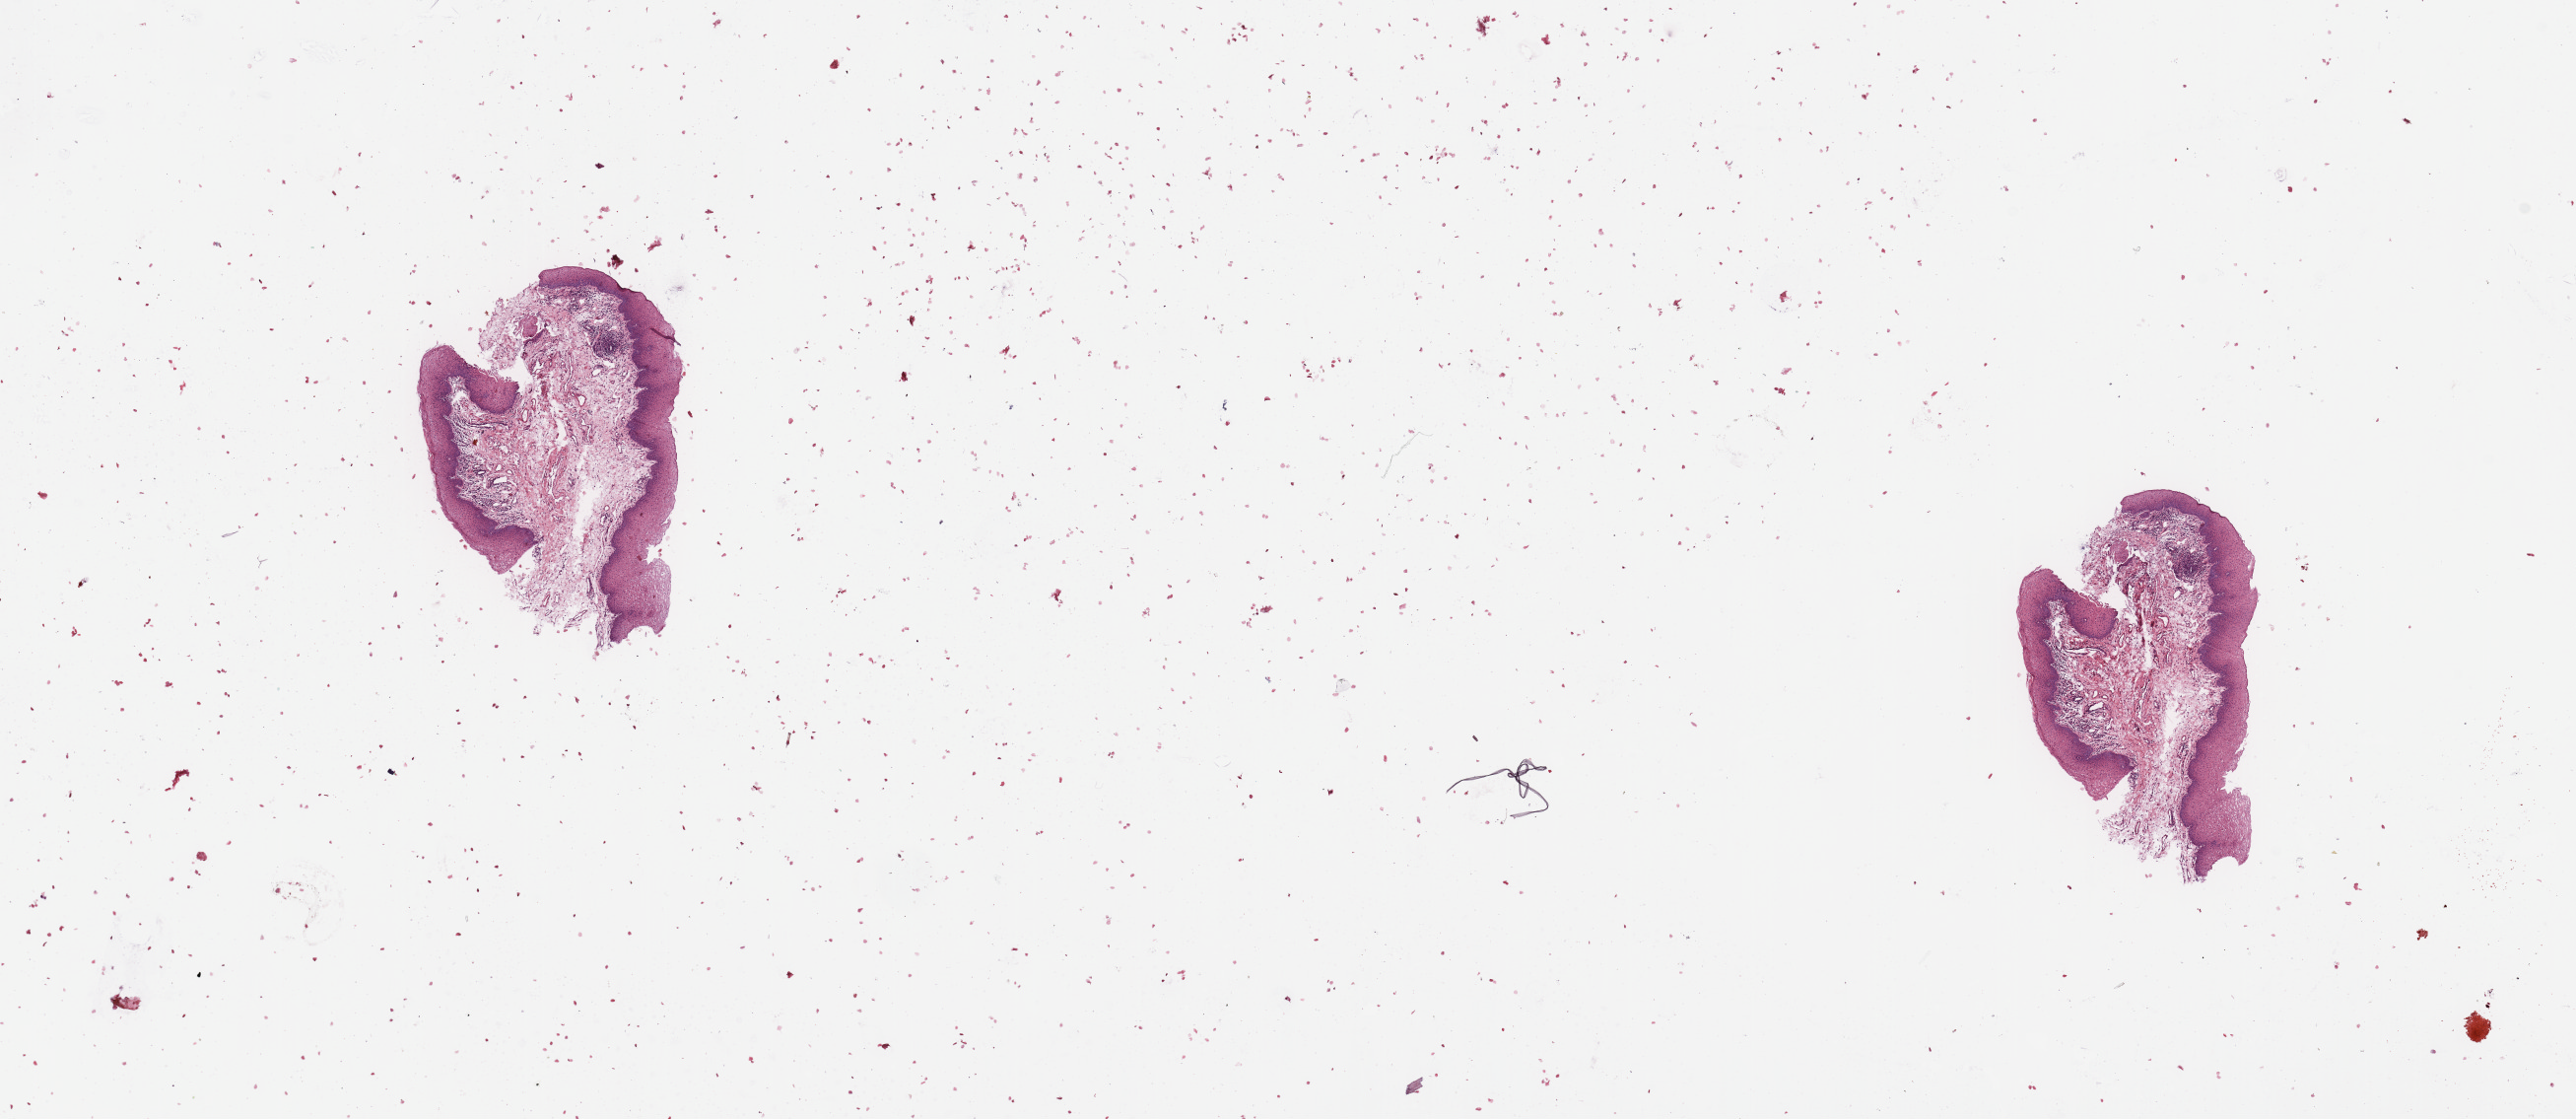
H&E whole-slide image, whole scanned area (about 20.7 x 9.0 mm) shown as a low-resolution overview. Normal (non-tumour) tissue sample, head and neck. Patient: male, age 64 years.
This section: normal (non-tumour) tissue from the same patient. Patient diagnosis: Squamous cell carcinoma, NOS (larynx, NOS).